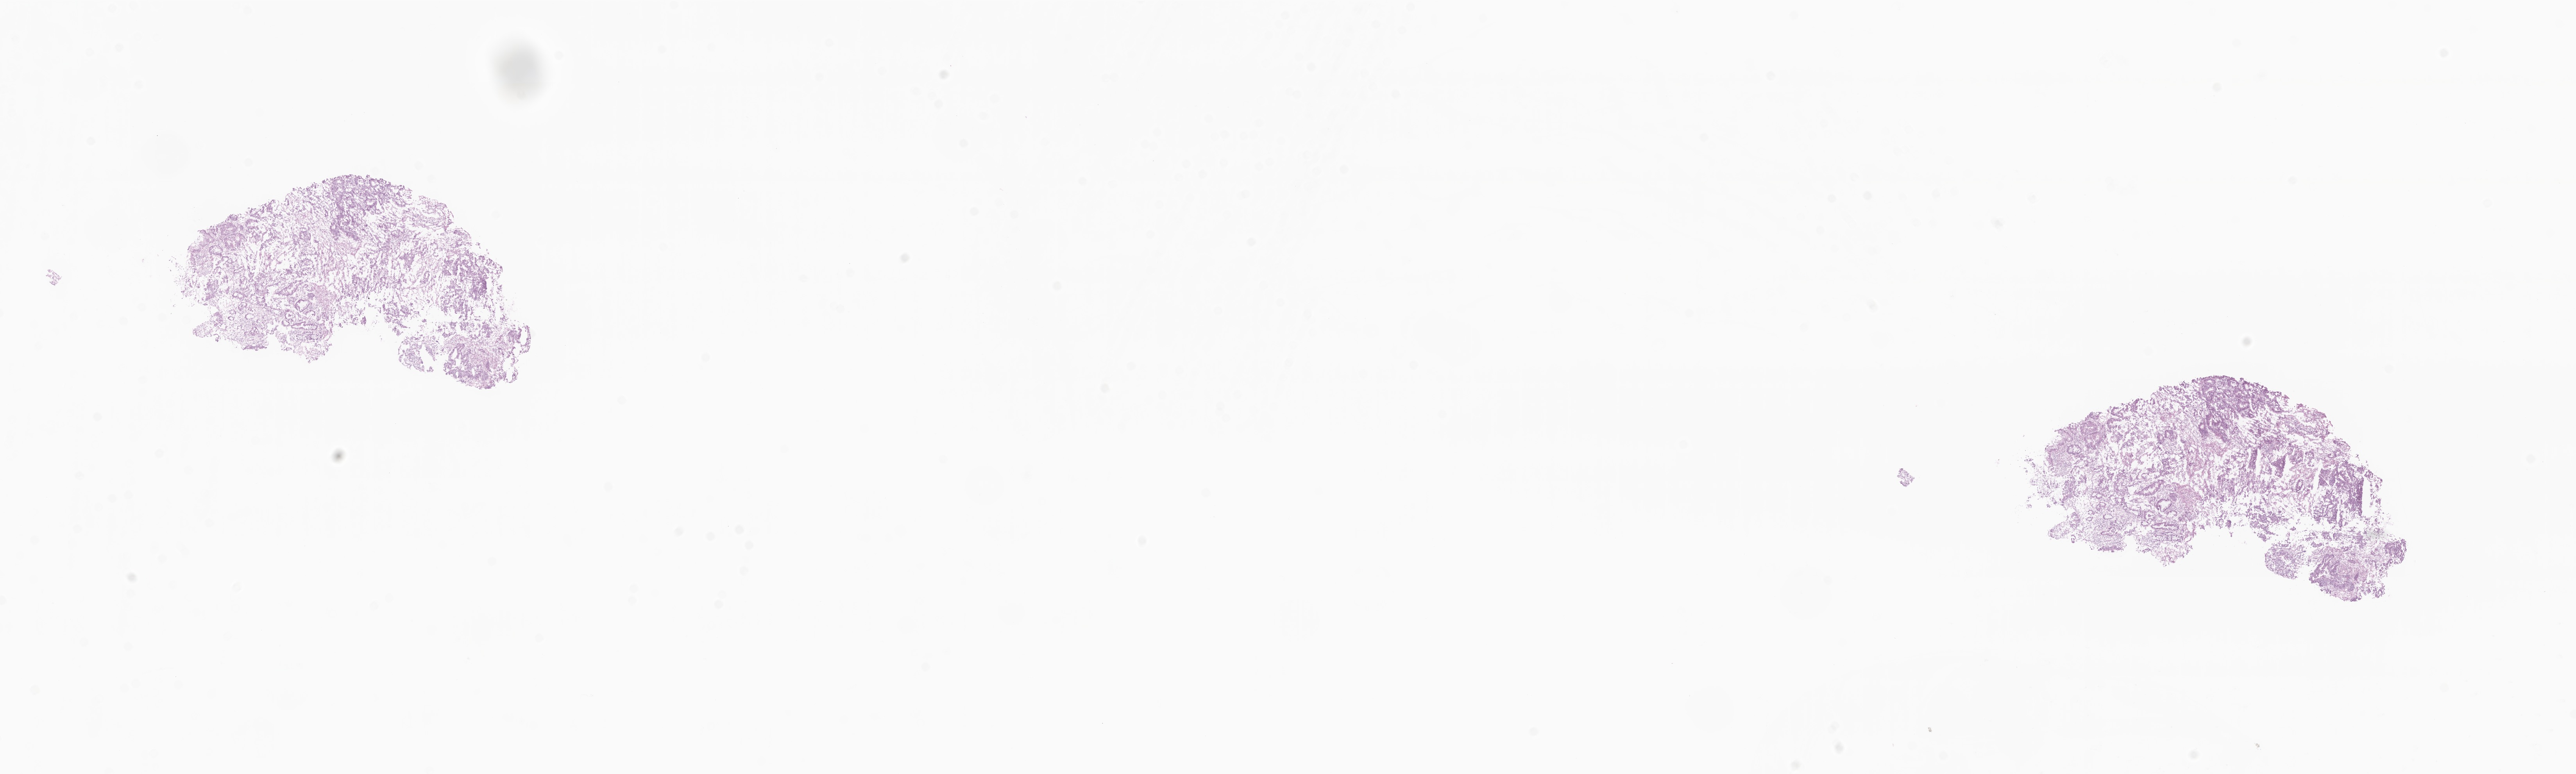
Whole-slide image, haematoxylin and eosin stain, whole scanned area (about 27.8 x 8.4 mm) shown as a low-resolution overview; frozen section; primary tumor; anatomic site: rectum. Patient sex: male. Tumor grade: G2 (moderately differentiated). Pathologist review of this section (percent, as recorded): tumor cells 100%, tumor nuclei 75%, stromal cells 0%, necrosis 0%, normal cells 0%. Inflammatory infiltration, as recorded: lymphocyte infiltration 0%, monocyte infiltration 0%, neutrophil infiltration 0%.
* diagnosis: Adenocarcinoma, NOS
* AJCC pathologic stage: Stage IIA